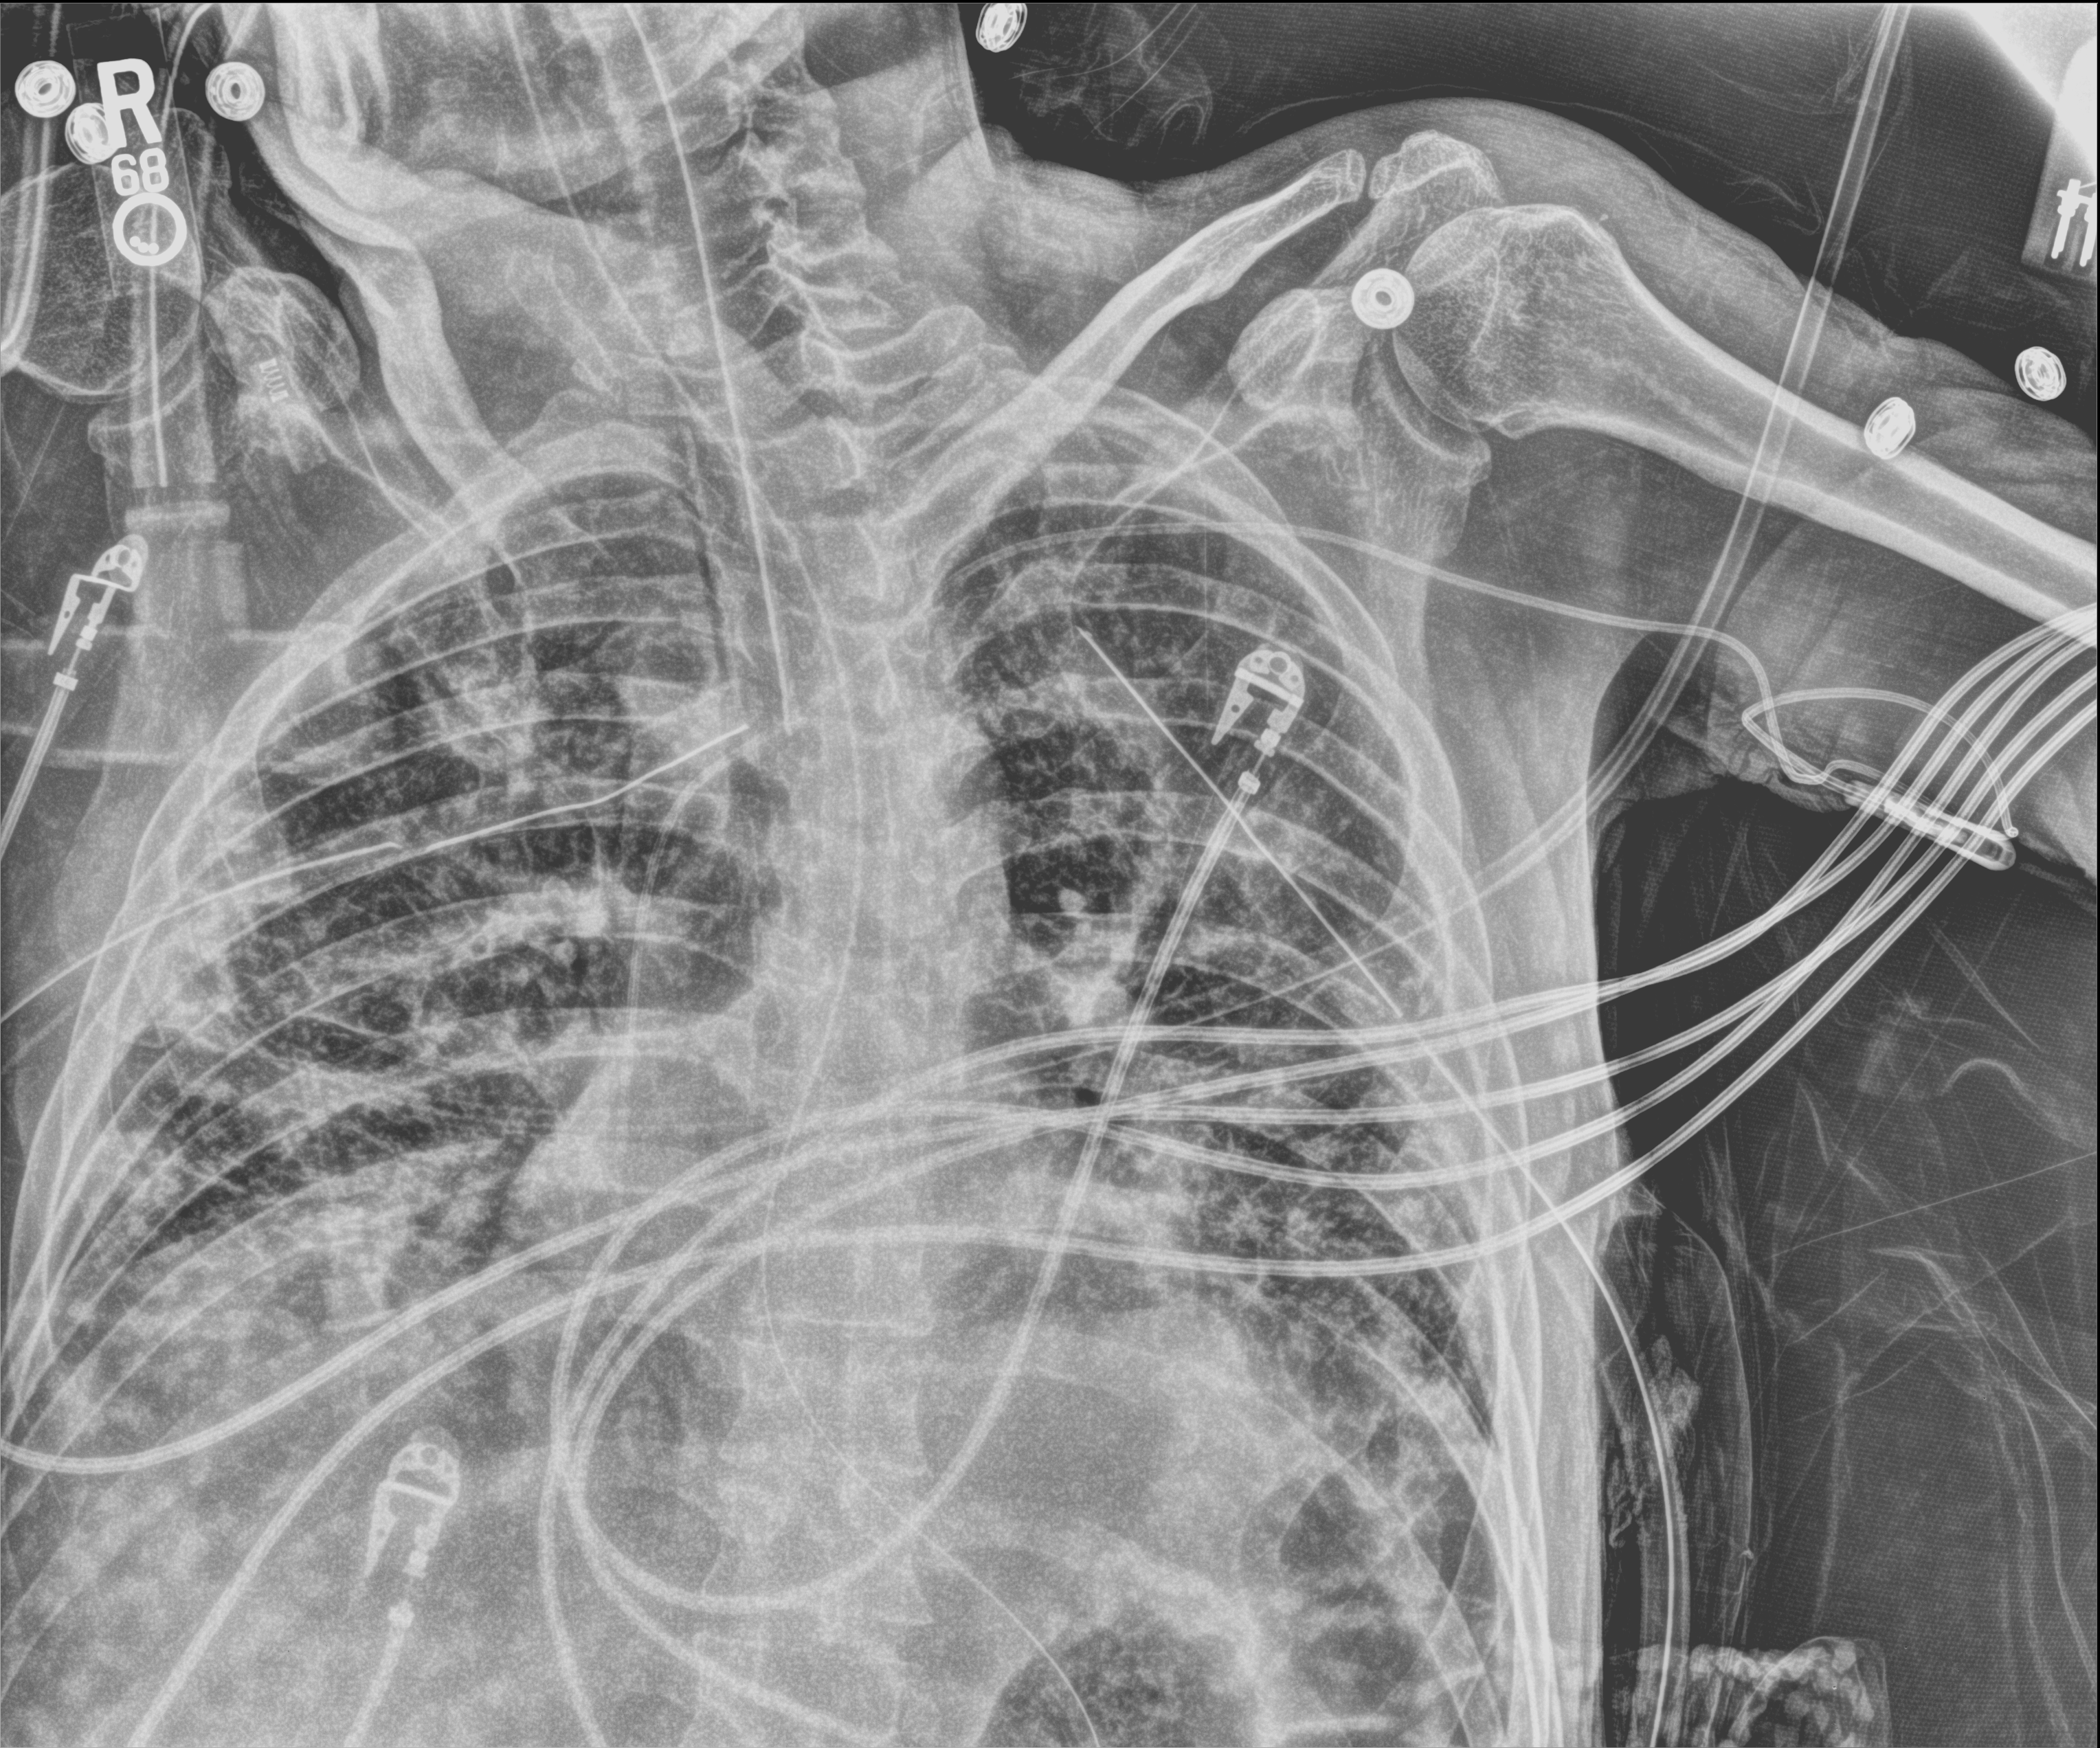
Portable chest radiograph, anteroposterior (AP) projection. Male patient hospitalised with COVID-19, age 18–59 years.
From the hospital-stay record, not from the radiograph (when in the stay this image was taken is not recorded): mechanically ventilated during this hospital stay: yes; other chronic lung disease (admission record): no; diabetes (admission record): yes.